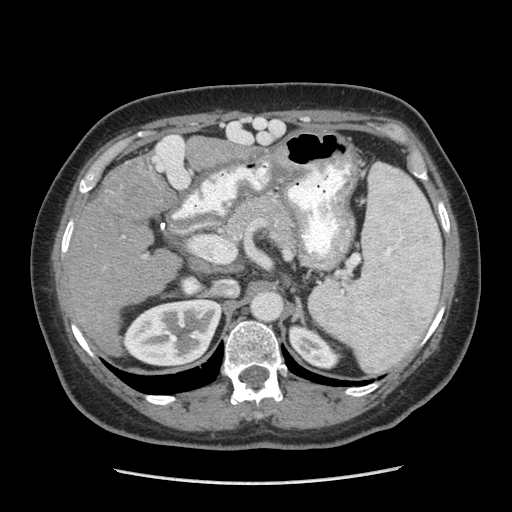
Contrast-enhanced abdominal CT (liver protocol), one axial slice. Slice 149 of 185 in the series (ordered by position). Reconstruction kernel STANDARD. 140 kVp. Soft-tissue window (W 400 / L 40 HU). 512 × 512 image matrix. From the clinical record (not read from this slice): diagnosis: hepatocellular carcinoma (patient treated with transarterial chemoembolisation; whether this scan precedes or follows treatment is not stated here); TNM stage (as recorded): Stage-I; Child-Pugh class: A; tumour differentiation: poorly differentiated; tumour nodularity: uninodular.
Outlined on this slice (semi-automatic segmentation, software-assisted and operator-edited):
- liver parenchyma outside the tumour (the mass and vessels are separate outlines, so this box may not span the whole liver): bounding box [x1, y1, x2, y2] px = [62, 134, 186, 346]
- mass: [102, 158, 171, 220]
- liver vessels: [70, 135, 185, 258]